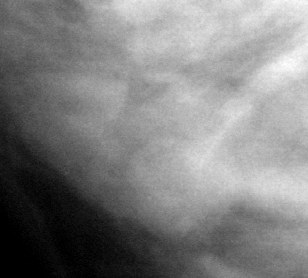
Region of interest cut from a scanned film mammogram (one marked finding); right breast; MLO view.
Finding: mass, shape oval, margins circumscribed; BI-RADS assessment category 4; pathology result (as recorded, not read from the image): benign.